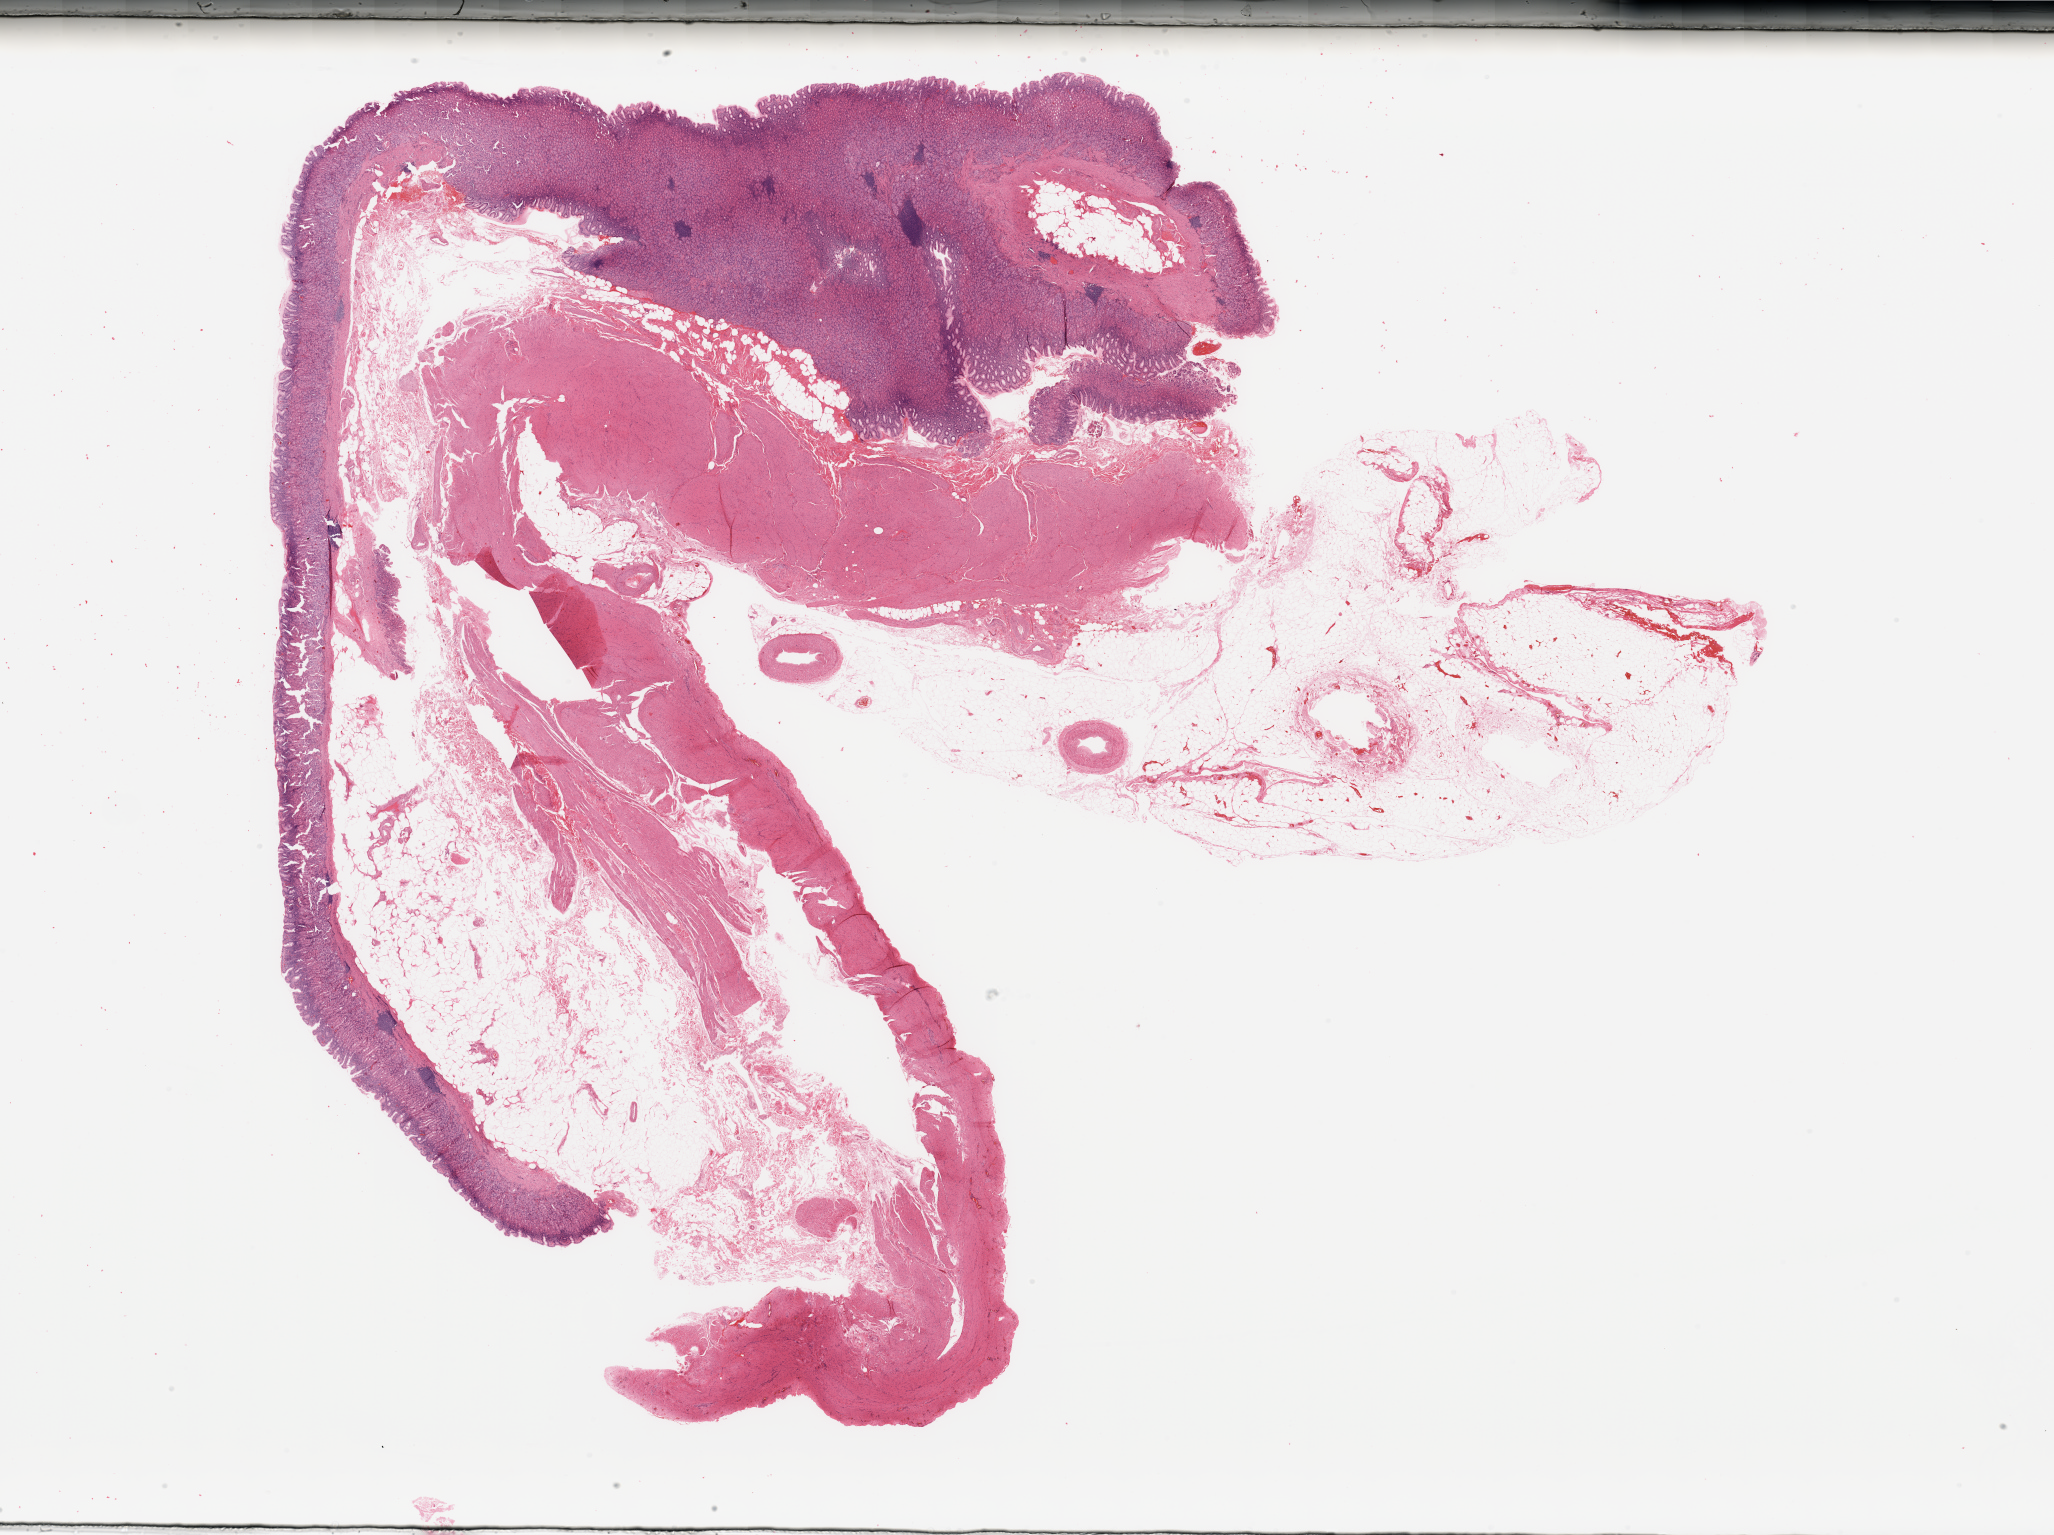
Digitized H&E-stained tissue section (whole slide), a low-resolution overview of the entire scanned area, about 32.5 x 24.3 mm (slide scanned at 20x). Patient: female, age 73 years.
Patient diagnosis (cohort enrolment): sarcoma (site not recorded at cohort level).